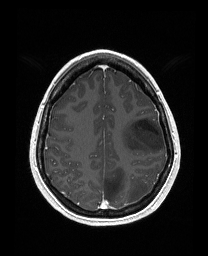
Brain MRI from a brain-tumour surgery series, one axial slice. Slice 118 of 176 in the series (ordered by position). T1-weighted post-contrast. 208 × 256 image matrix, field of view 203 × 250 mm. Case-level facts recorded for this patient, not image findings: histopathology: Astrocytoma; WHO grade: 3; IDH mutation: yes; tumour location: Left Frontal.
Annotated regions visible in this slice (expert manual segmentation):
- tumour: bounding box <120,117,165,153> (left, top, right, bottom; pixels)